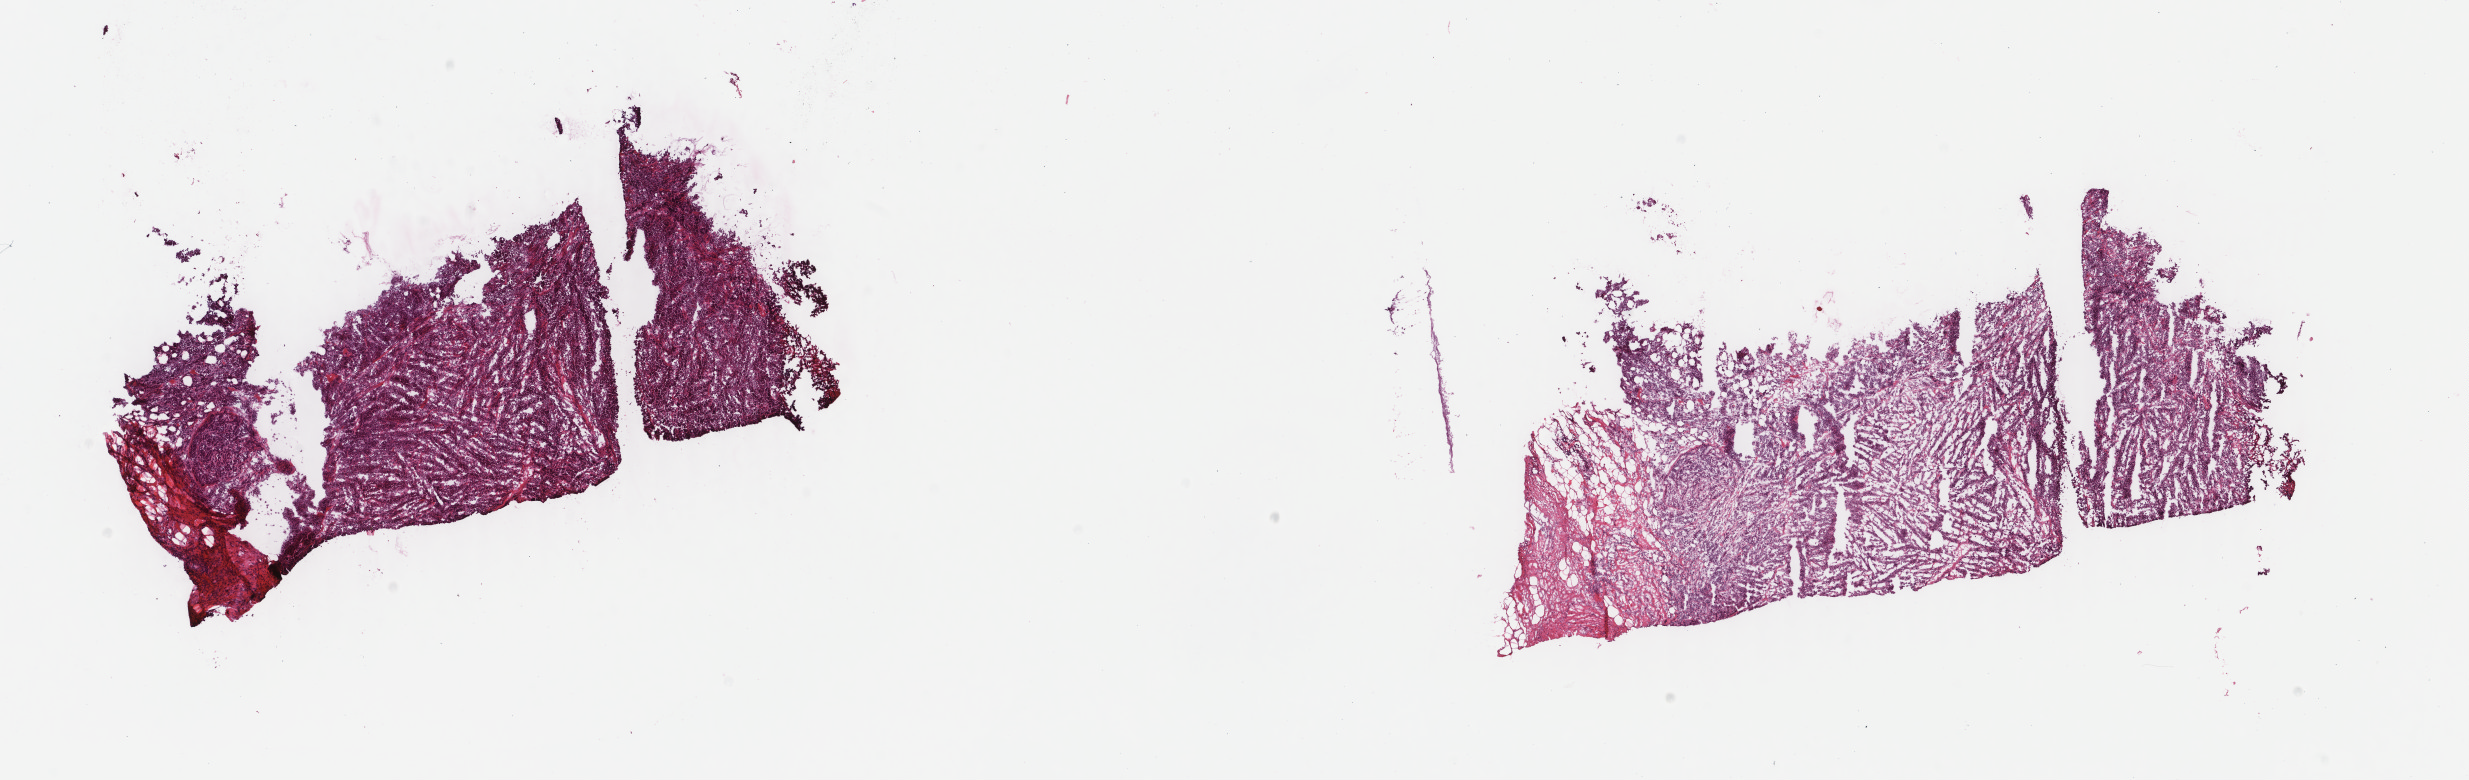
Hematoxylin and eosin (H&E) stained whole-slide image, shown as a low-resolution overview of the whole scanned area (about 19.6 x 6.2 mm); frozen section from the top of the tissue portion; breast, primary tumour sample. Female patient; age at initial diagnosis 50 years. Slide review estimates, as recorded: tumour cells 80%, tumour nuclei 90%, normal cells 0%, stromal cells 20%, necrosis 0%. Inflammatory infiltration, as recorded: lymphocyte infiltration 0%, monocyte infiltration 0%, neutrophil infiltration 0%.
AJCC pathologic stage: IIIA. Laterality: left. TNM: T1 N2 M0. Histologic diagnosis: Infiltrating duct carcinoma, NOS.